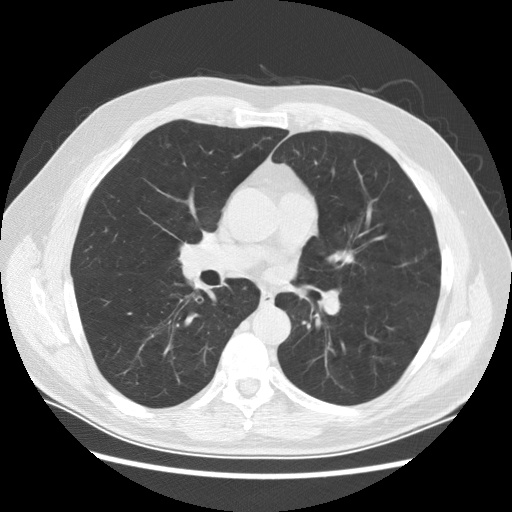
Axial slice from a low-dose chest CT screening exam. Baseline annual screen. Lung window (W 1500 / L -600 HU). 2.5 mm slice thickness. 120 kVp. Slice 114 of 241 in the series. Male participant, aged 61 years at enrolment. Former smoker at enrolment.
• Expert reader's lesion annotation, box from (x=225, y=275) to (x=258, y=311) px.
• Screening reader's record for this exam: no non-calcified nodule ≥4 mm recorded.
• Later outcome: lung cancer diagnosed 756 days after this screen — squamous cell carcinoma, keratinizing, NOS, right lower lobe, stage IIIB (AJCC 6th edition), 40 mm at pathology.